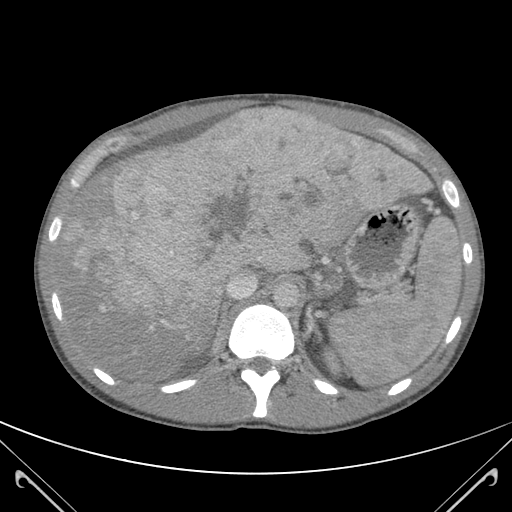
Contrast-enhanced abdominal CT (liver protocol), one axial slice; position 82 of 118 along the scan axis; 120 kVp; soft-tissue window (W 400 / L 40 HU); 3 mm slice thickness; 512 × 512 image matrix, field of view 380 × 380 mm. From the clinical record (not read from this slice): diagnosis: hepatocellular carcinoma (patient treated with transarterial chemoembolisation; whether this scan precedes or follows treatment is not stated here); TNM stage (as recorded): Stage-IIIB; Child-Pugh class: A; tumour nodularity: uninodular.
Annotated regions visible in this slice (semi-automatic segmentation, software-assisted and operator-edited):
- abdominal aorta: bounding box <273,283,298,308> (left, top, right, bottom; pixels)
- liver parenchyma outside the tumour (the mass and vessels are separate outlines, so this box may not span the whole liver): <59,113,422,378>
- mass: <90,116,415,334>
- liver vessels: <66,114,416,311>